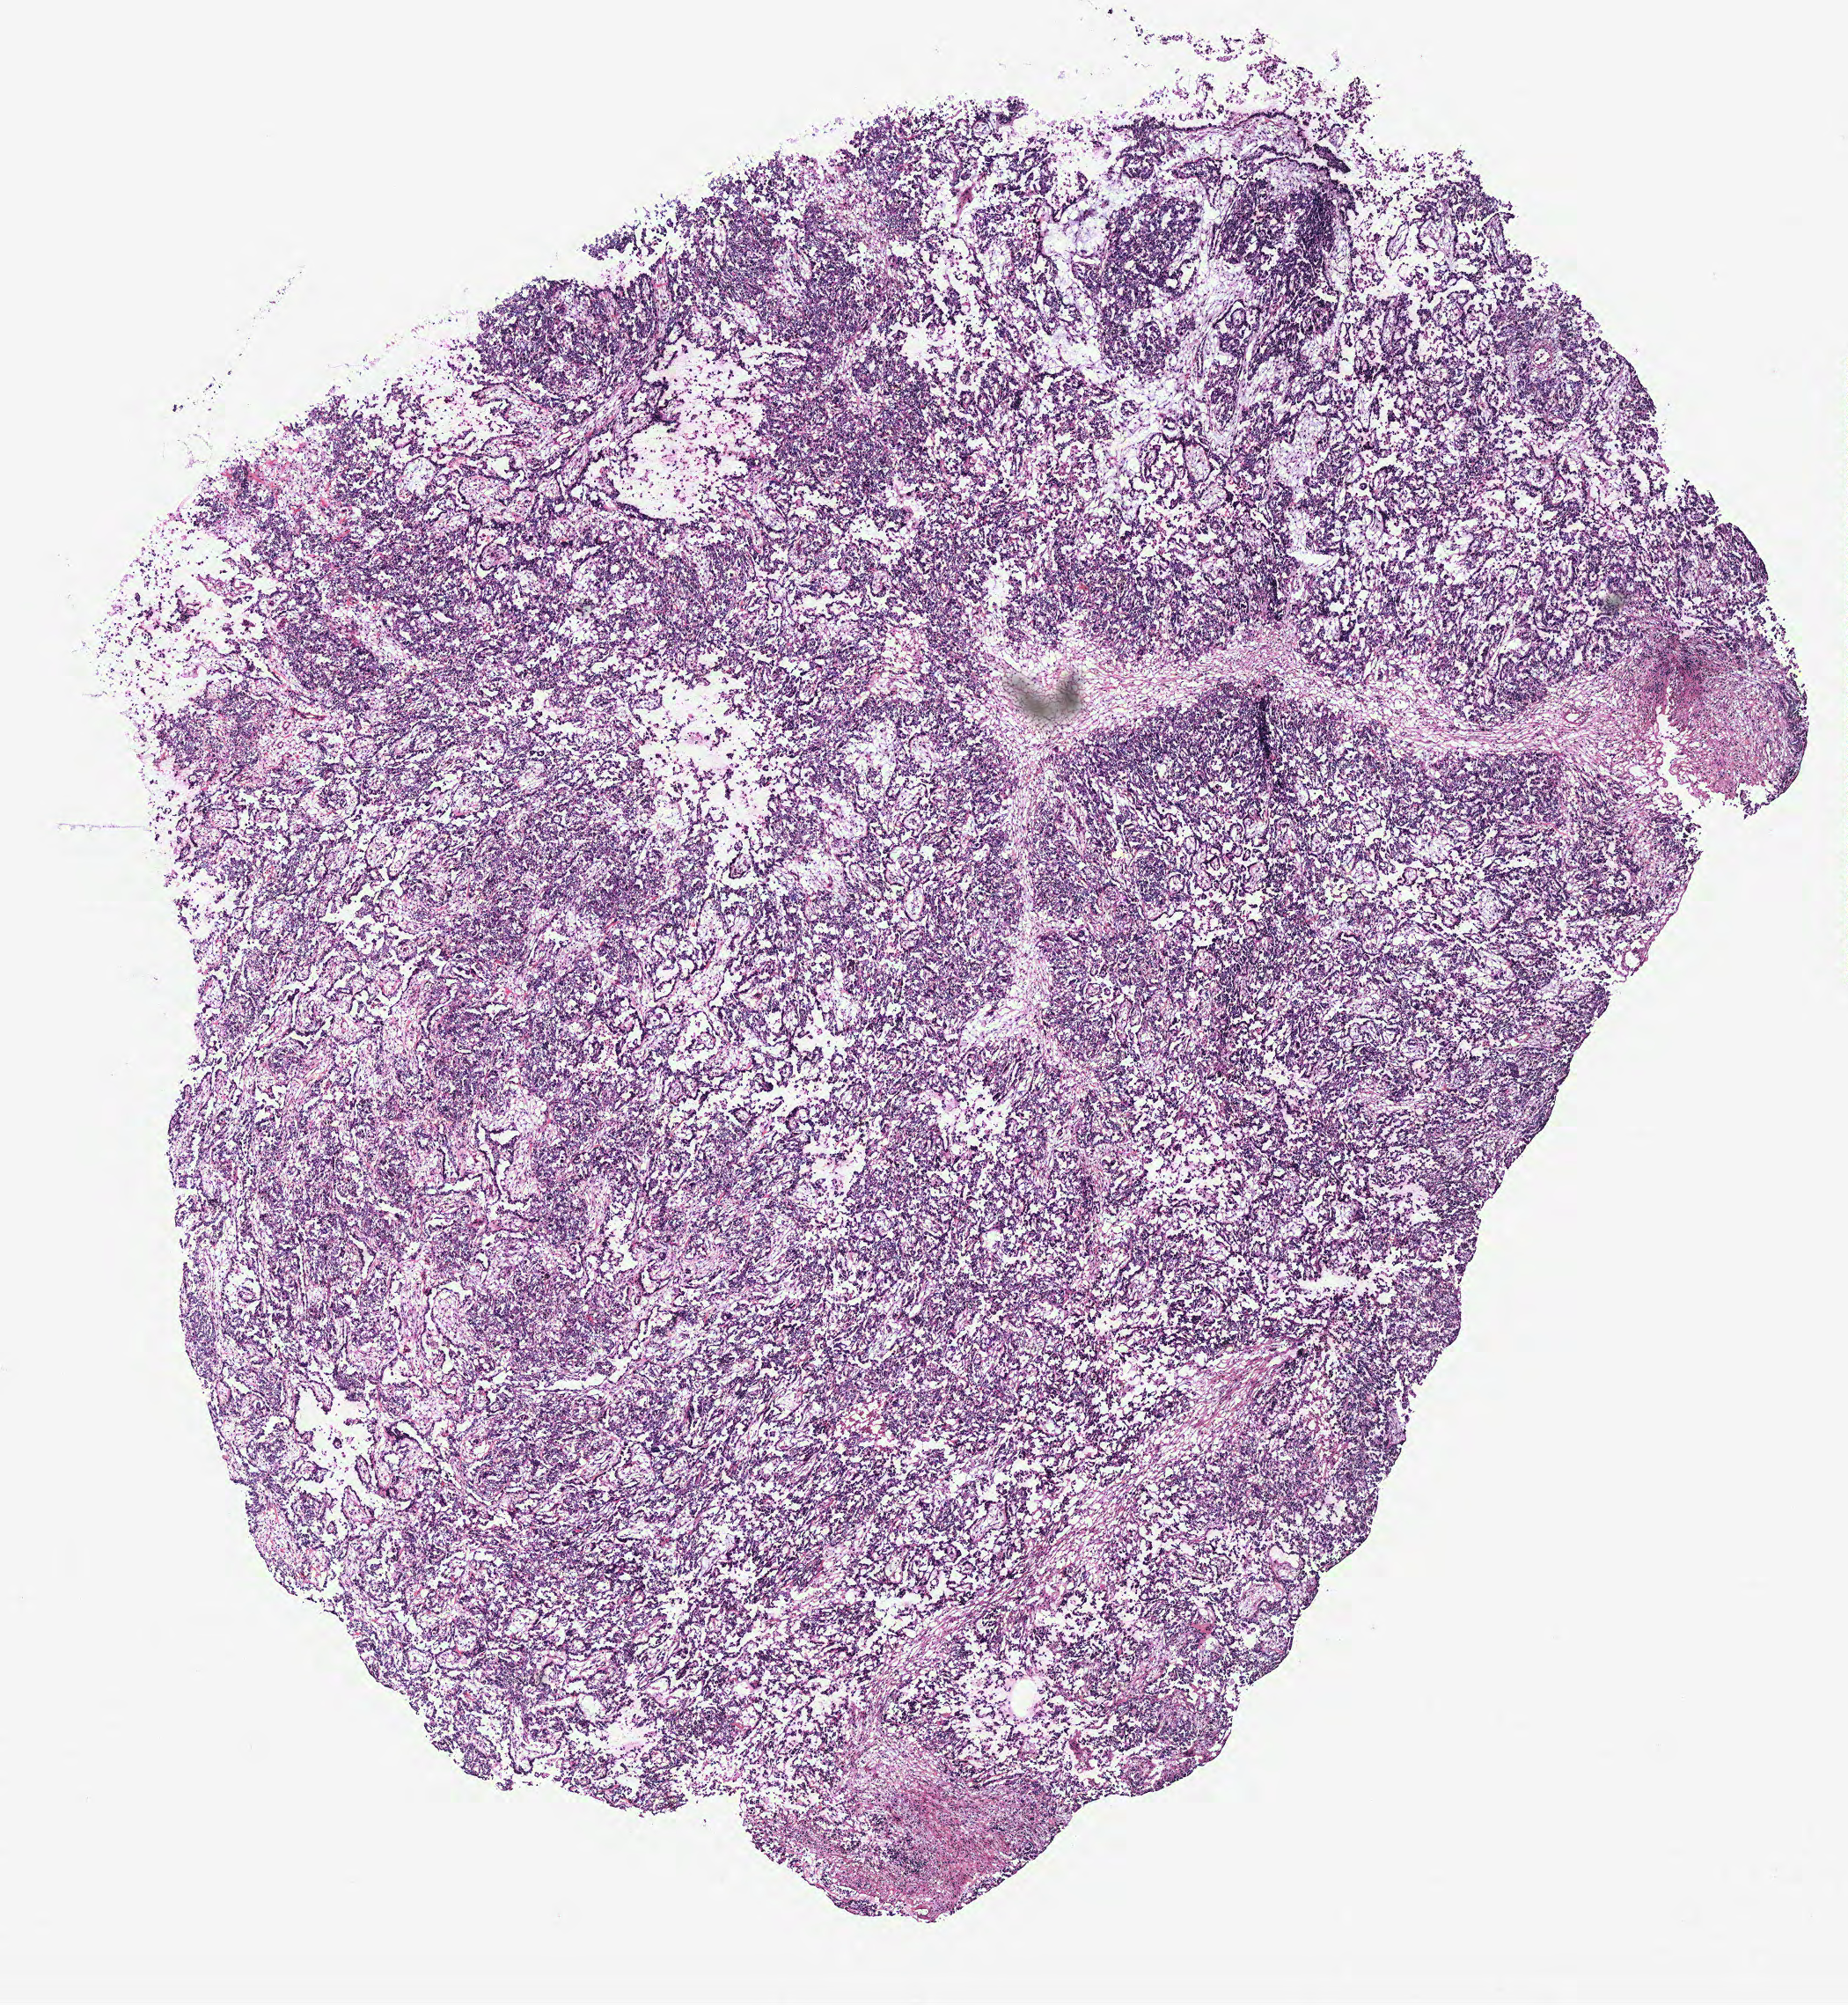
Digitized Hematoxylin and eosin (H&E) stained tissue section (whole slide), a low-resolution overview of the entire scanned area, about 8.4 x 9.1 mm (acquisition: 40x scan); ovary, tumour tissue. Patient: female, age 74 years.
- primary tumour site (as recorded): peritoneum
- diagnosis: Serous adenocarcinoma, NOS (peritoneum, NOS)